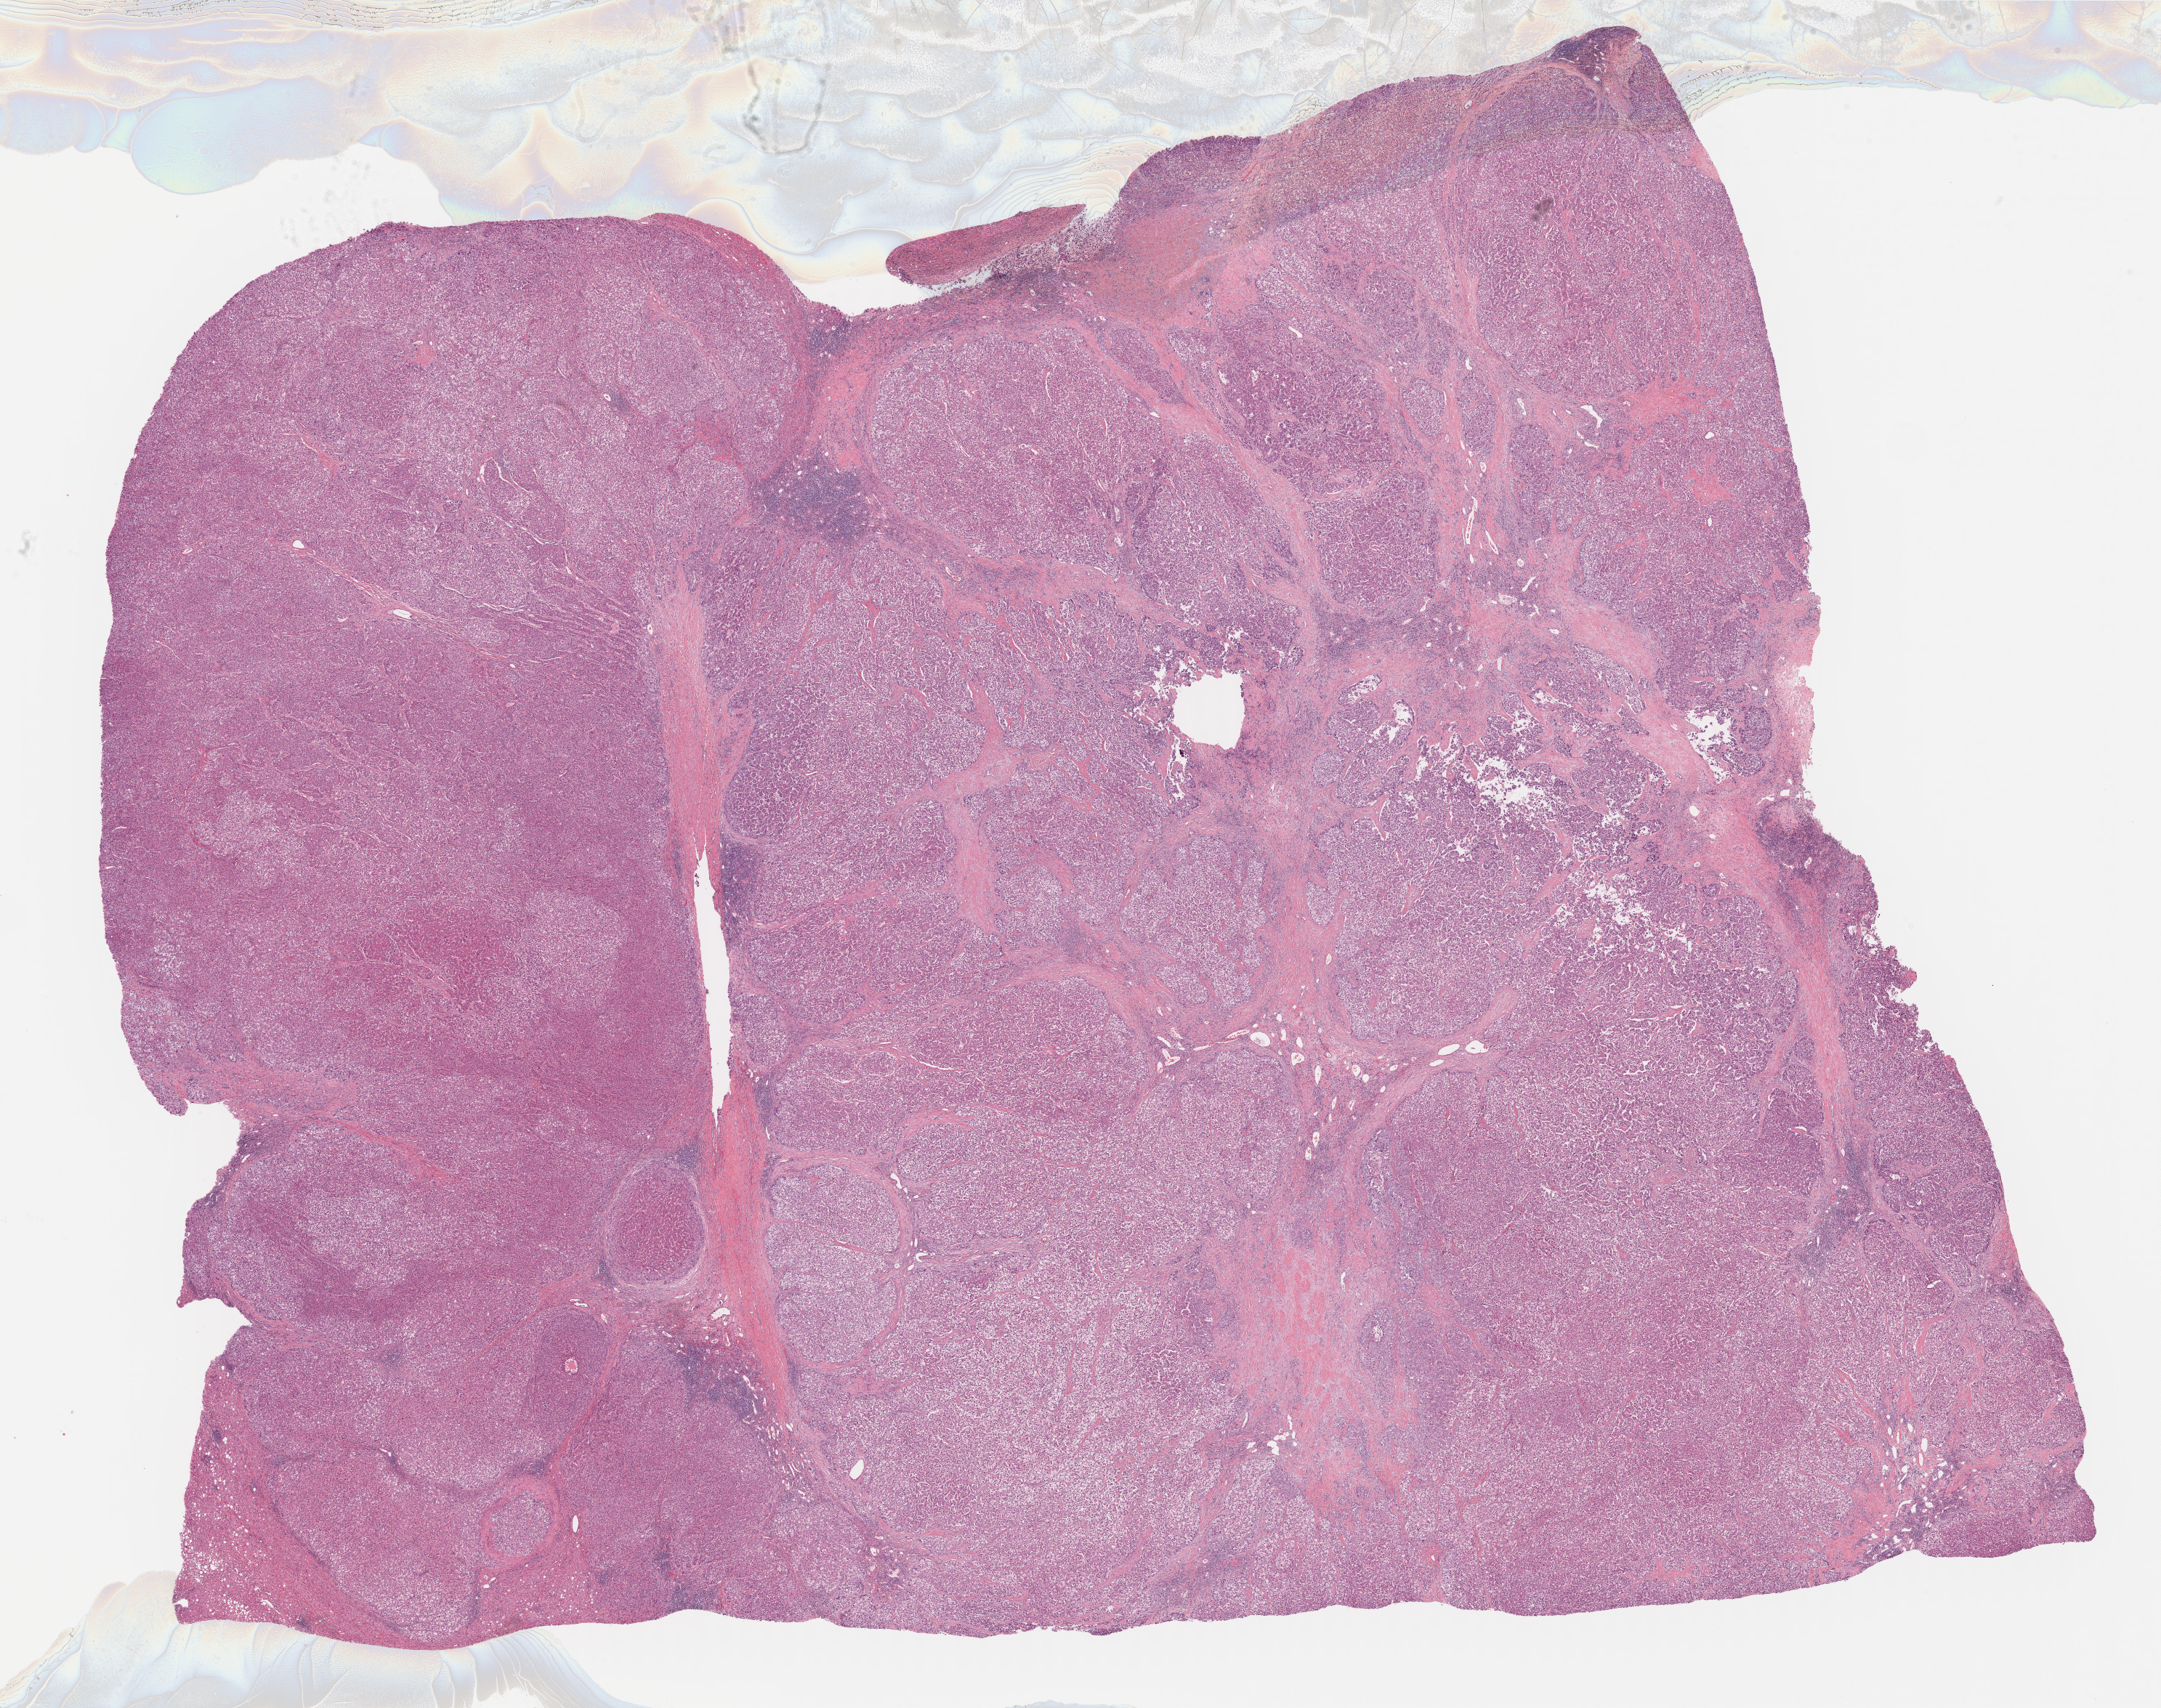
Hematoxylin and eosin (H&E) stained whole-slide image — whole scanned area (about 24.1 x 19.0 mm, slide scanned at 40x) shown as a low-resolution overview, formalin-fixed paraffin-embedded (FFPE) diagnostic section, liver, primary tumour sample. Female patient; age at initial diagnosis 54 years. Histologic grade: G2 (moderately differentiated).
TNM: T2 N0 M0. Pathologic diagnosis: Hepatocellular carcinoma, NOS. AJCC pathologic stage: II (7th edition).